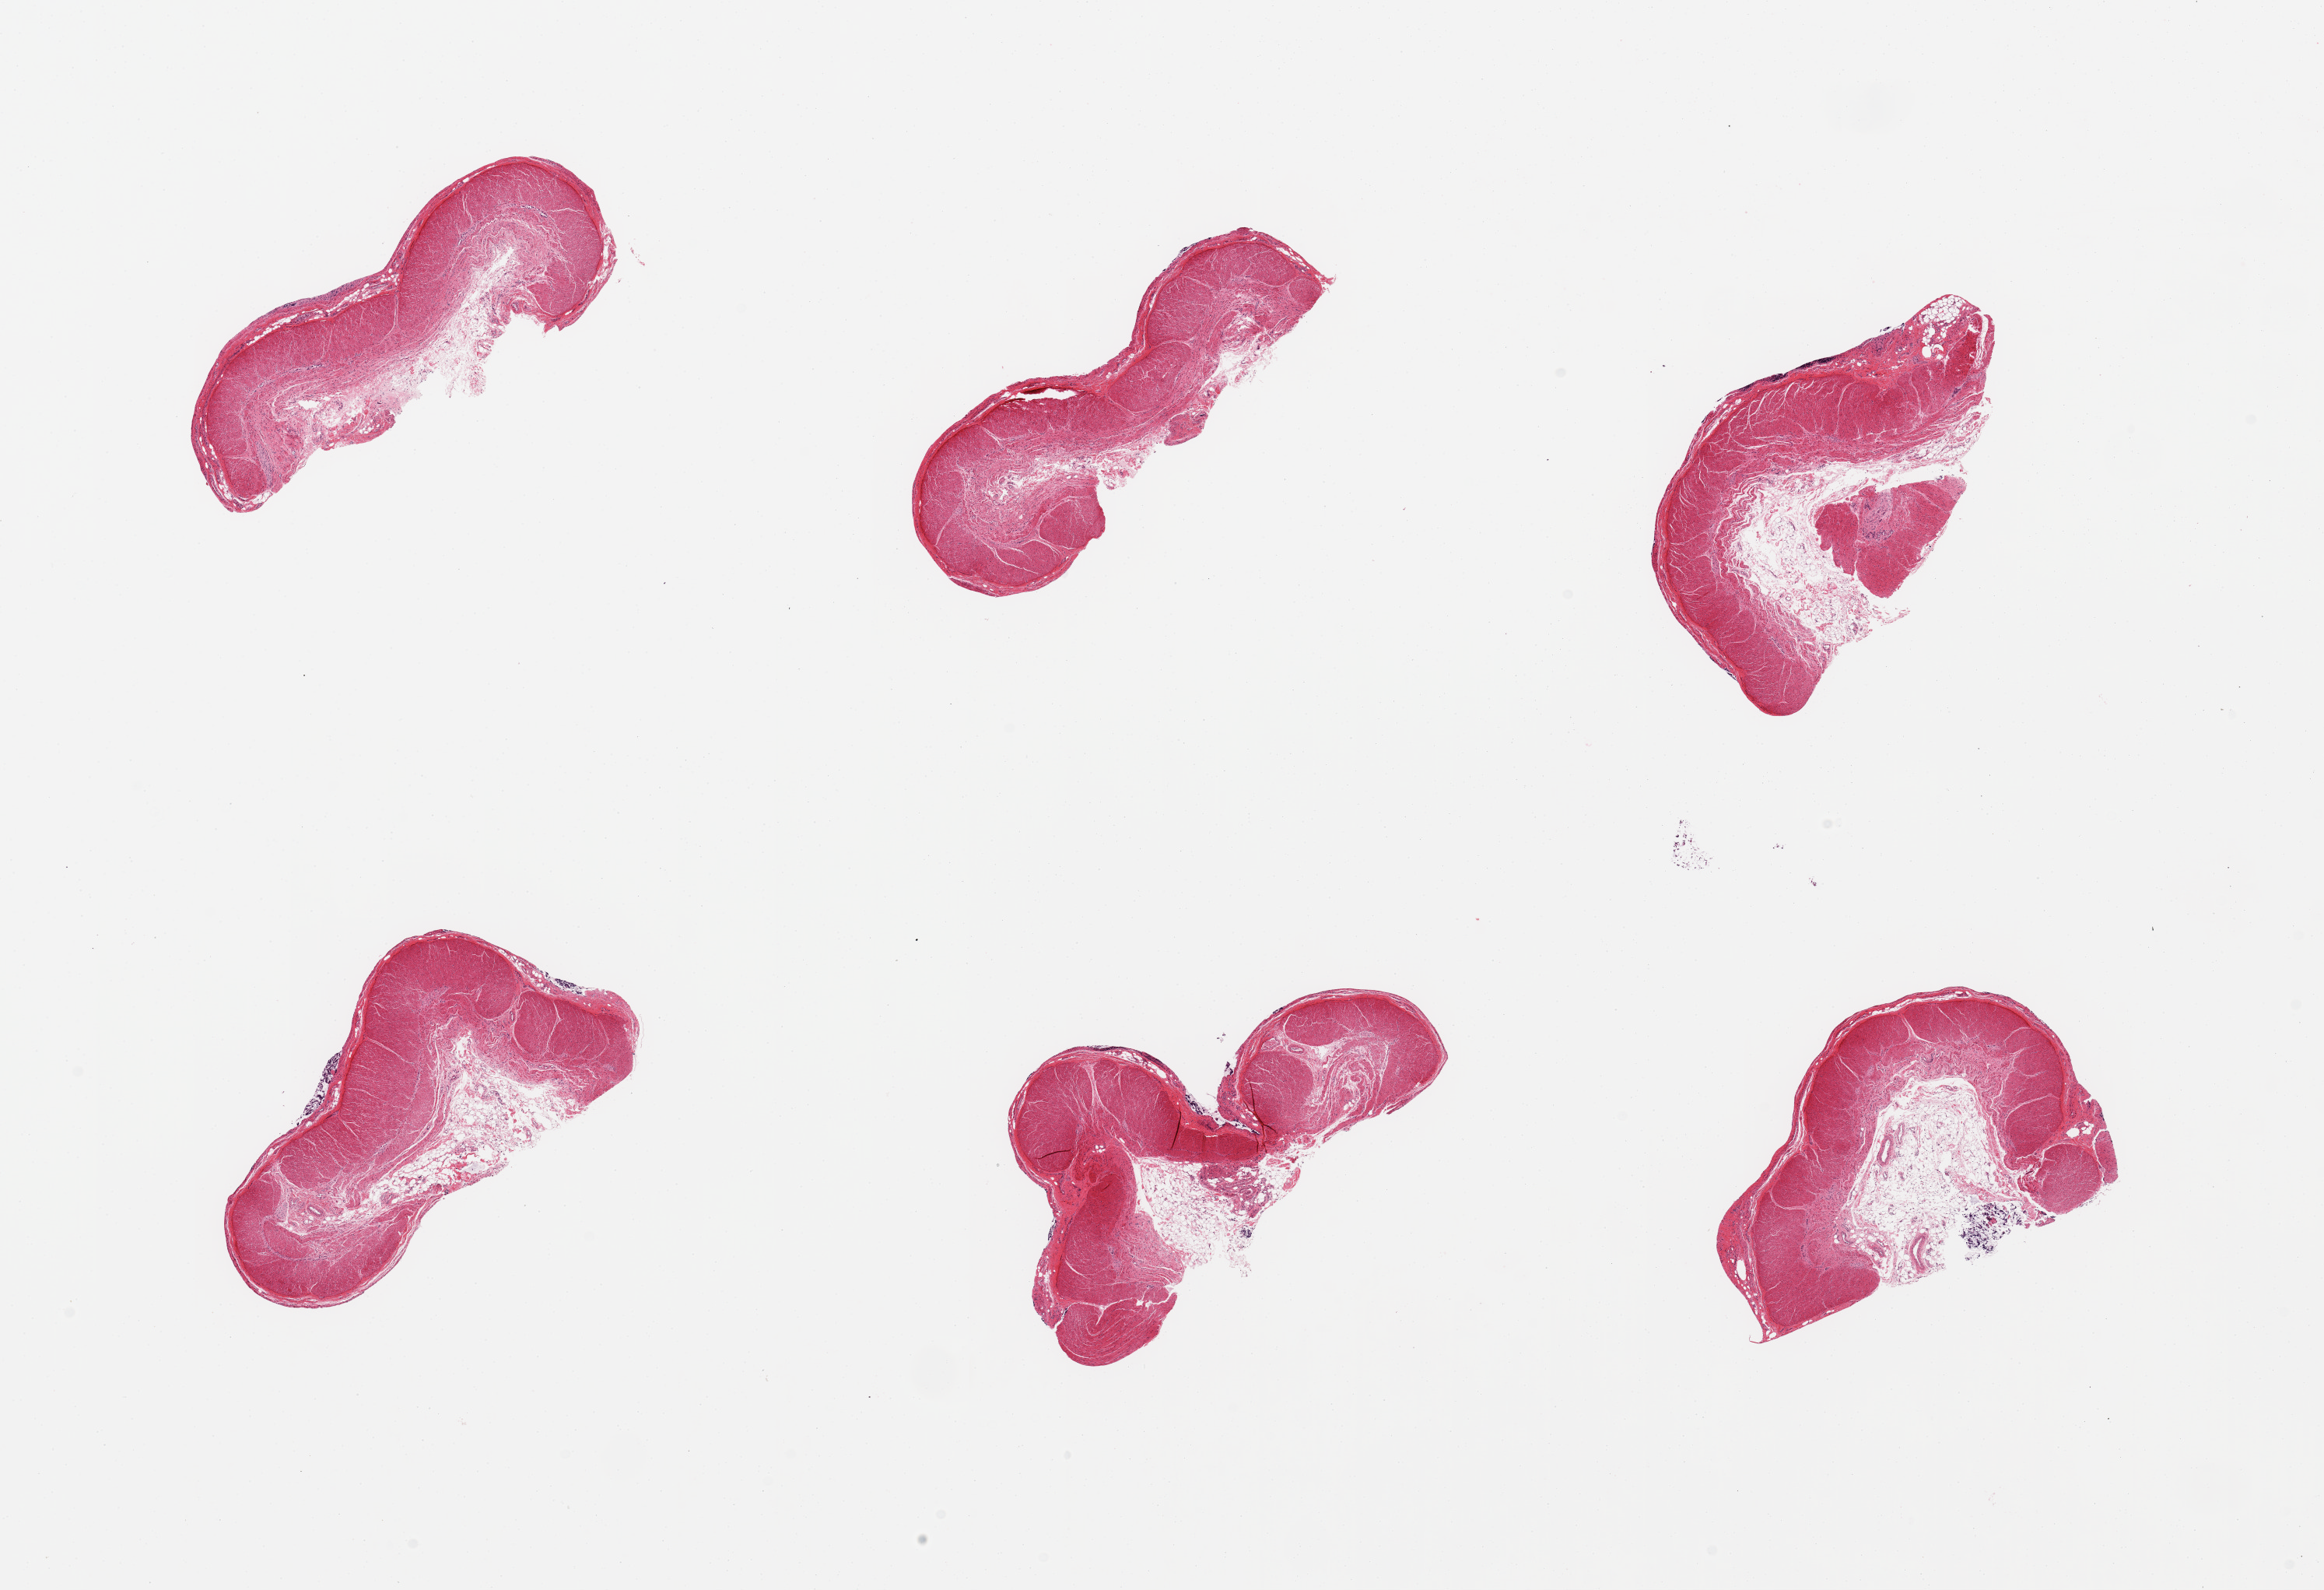
H&E whole-slide image, low-resolution overview of the scanned area, about 23.6 x 16.2 mm (acquisition: 20x scan), PAXgene-fixed paraffin-embedded (PFPE) section, target tissue: sigmoid colon, tissue donor sample. Donor sex: female.
- pathologist's review note for this sample: 6 pieces; 10% to 30% submucosal fat present